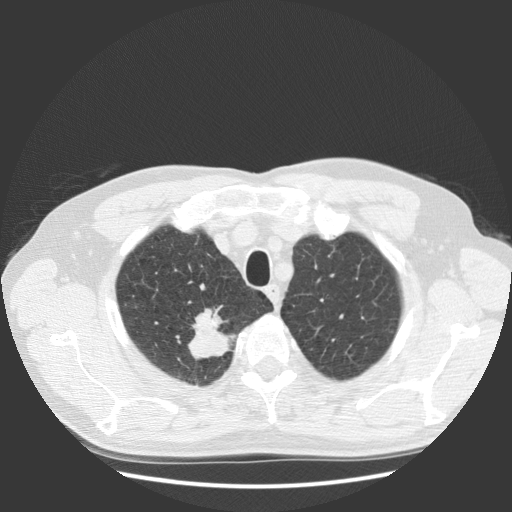
Low-dose screening chest CT, axial slice; baseline annual screen; lung window (W 1500 / L -600 HU); 2.5 mm slice thickness; standard (soft-tissue) reconstruction kernel (STANDARD); 512 × 512 image matrix. Male participant, aged 63 years at enrolment.
Lesion marked by an expert reader, bounding box <167,319,238,383> (left, top, right, bottom; pixels). The screening reader recorded 2 non-calcified nodules or masses ≥4 mm on this exam (right upper lobe, right upper lobe); which of them this box marks is not recorded. Lung cancer was diagnosed 30 days after this screen: squamous cell carcinoma, NOS, right upper lobe, stage IIIB (AJCC 6th edition), 35 mm at pathology.